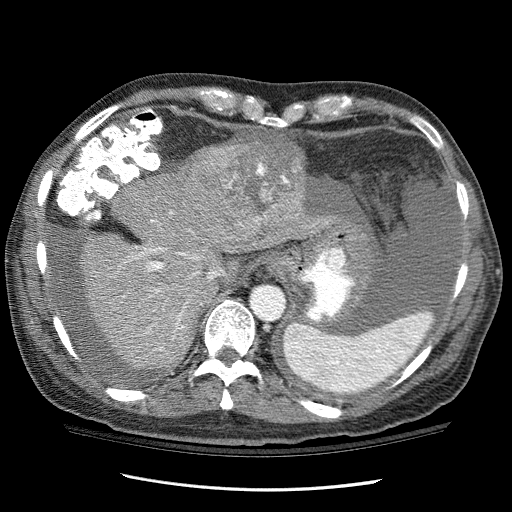
Contrast-enhanced abdominal CT (liver protocol), one axial slice; slice 85 of 114 in the series (ordered by position); 120 kVp; one of 3 acquisitions stored at this slice position; soft-tissue window (W 400 / L 40 HU); 2.5 mm slice thickness; 512 × 512 image matrix. Case-level facts recorded for this patient, not image findings: diagnosis: hepatocellular carcinoma (patient treated with transarterial chemoembolisation; whether this scan precedes or follows treatment is not stated here); TNM stage (as recorded): Stage-I; Child-Pugh class: C; tumour differentiation: well differentiated; tumour nodularity: uninodular.
Structures marked on this image (semi-automatic segmentation, software-assisted and operator-edited):
- abdominal aorta: bounding box (x1, y1, x2, y2) in pixels: (251, 286, 285, 320)
- liver parenchyma outside the tumour (the mass and vessels are separate outlines, so this box may not span the whole liver): (58, 155, 332, 370)
- mass: (183, 129, 309, 247)
- liver vessels: (138, 211, 198, 338)